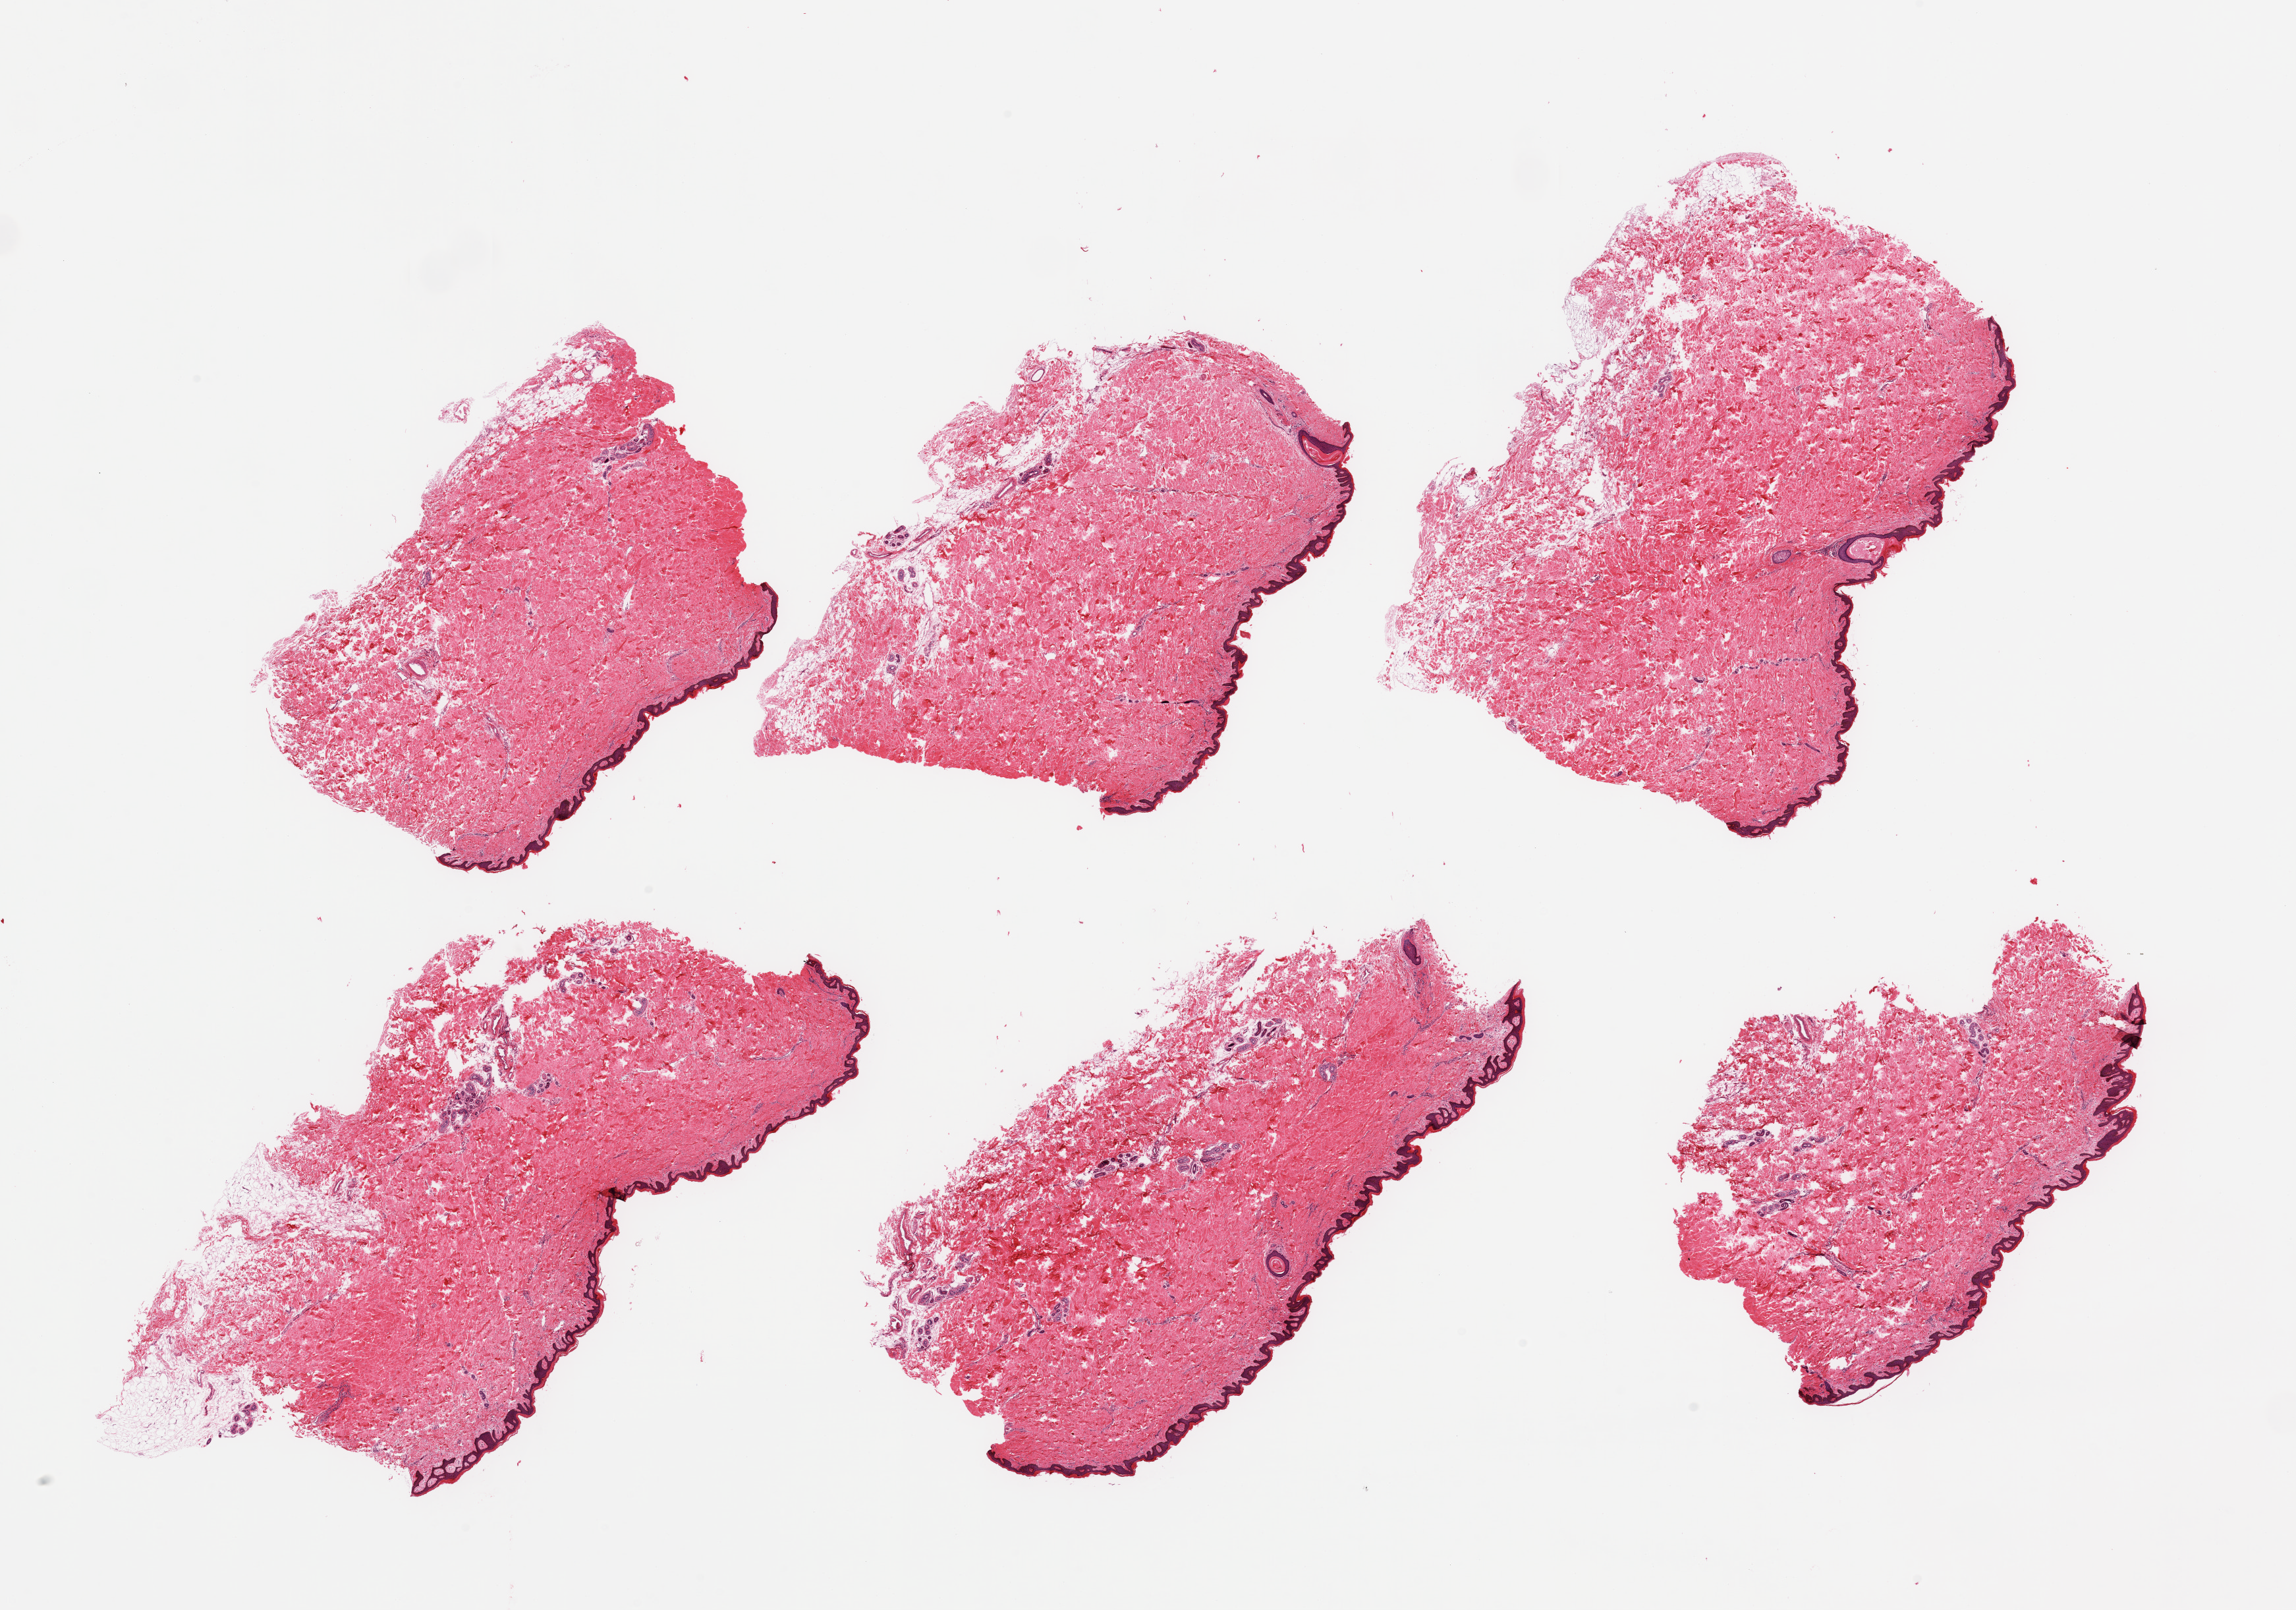
Whole-slide image, H&E stain, brightfield — a low-resolution overview of the entire scanned area, about 27.6 x 19.3 mm; PAXgene-fixed, paraffin-embedded tissue; sampled site (target tissue): skin of suprapubic region; tissue donor sample.
Review note (as recorded): 2 pieces, minimal dermal fat; squamous epithelium is ~50 microns.